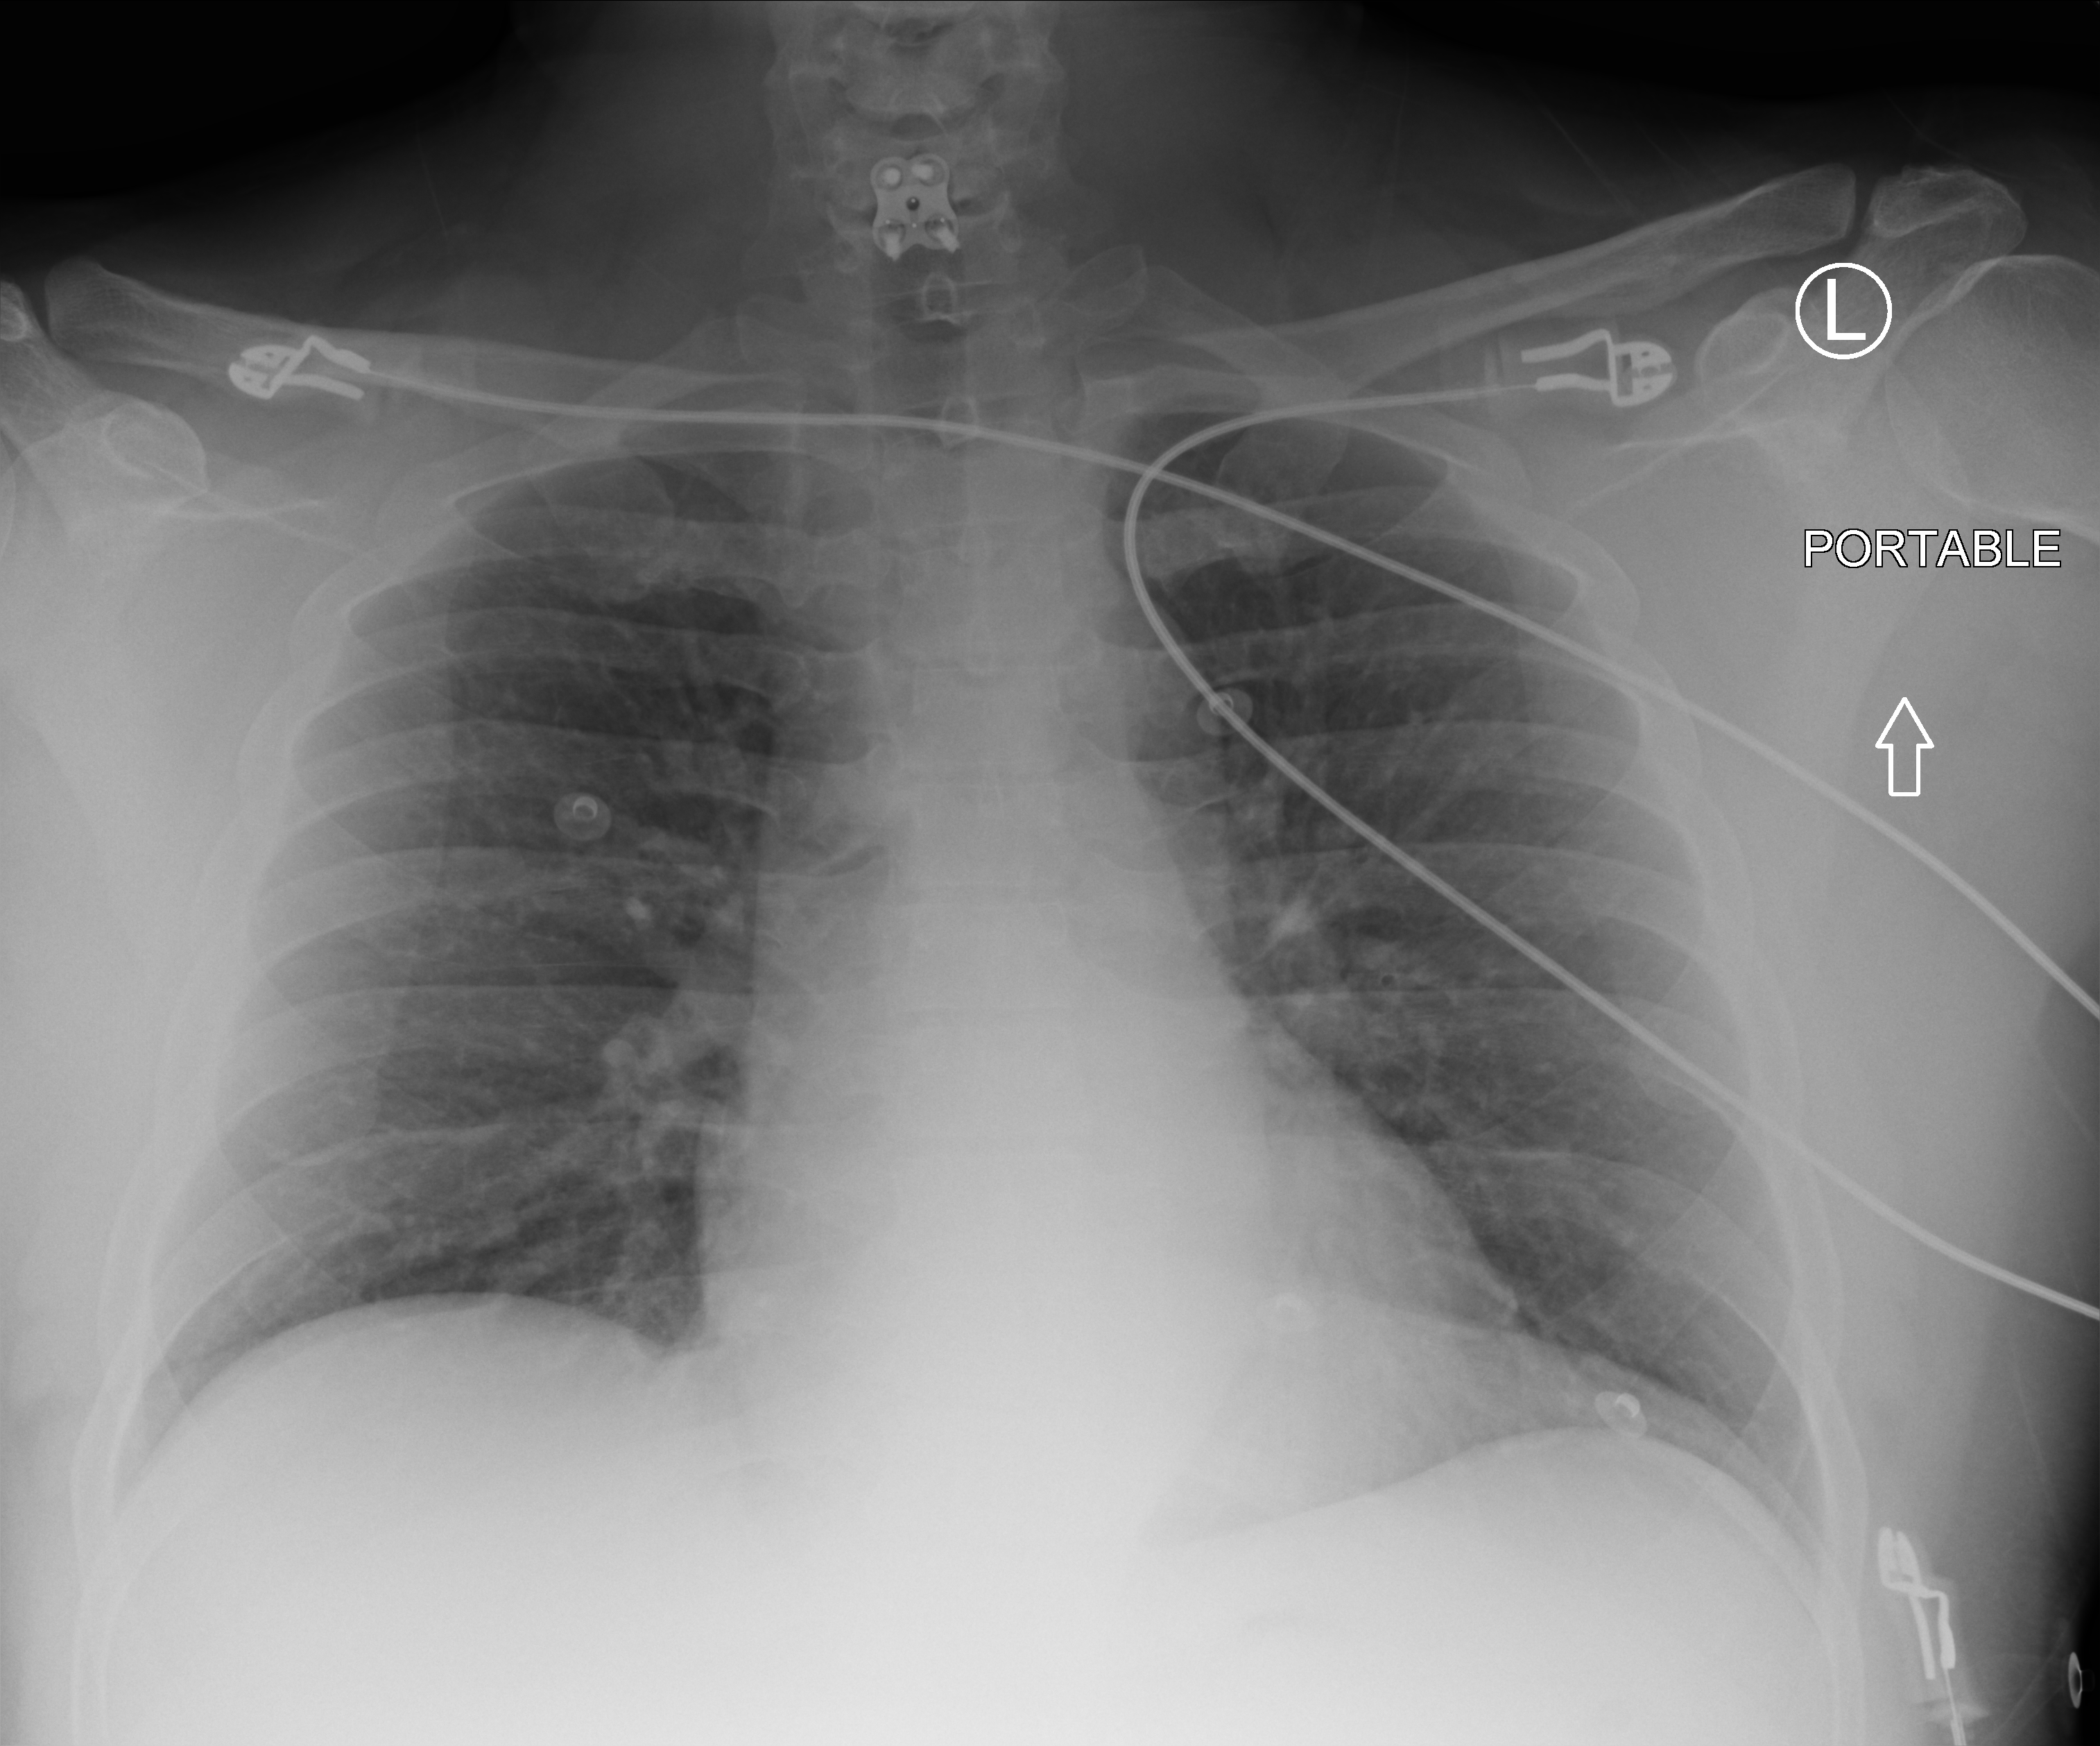
Bedside chest radiograph (computed radiography), anteroposterior (AP) projection. Patient hospitalised with COVID-19; male, aged 18–59 years.
From the hospital-stay record, not from the radiograph (when in the stay this image was taken is not recorded):
- admitted to intensive care during this hospital stay: no
- smoking status (admission record): never
- length of hospital stay: 1 day